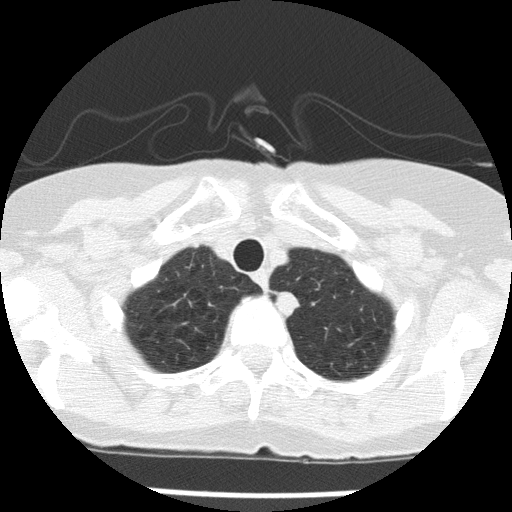
Low-dose screening chest CT, one axial slice; reconstruction kernel FC51; 120 kVp; lung window (W 1500 / L -600 HU); 2 mm slice thickness; 512 × 512 image matrix, field of view 276 × 276 mm.
Outlined on this slice (manually delineated by an expert):
- lesion 1 (tumor, upper lobe of left lung): bounding box (x1, y1, x2, y2) in pixels: (276, 292, 300, 319)